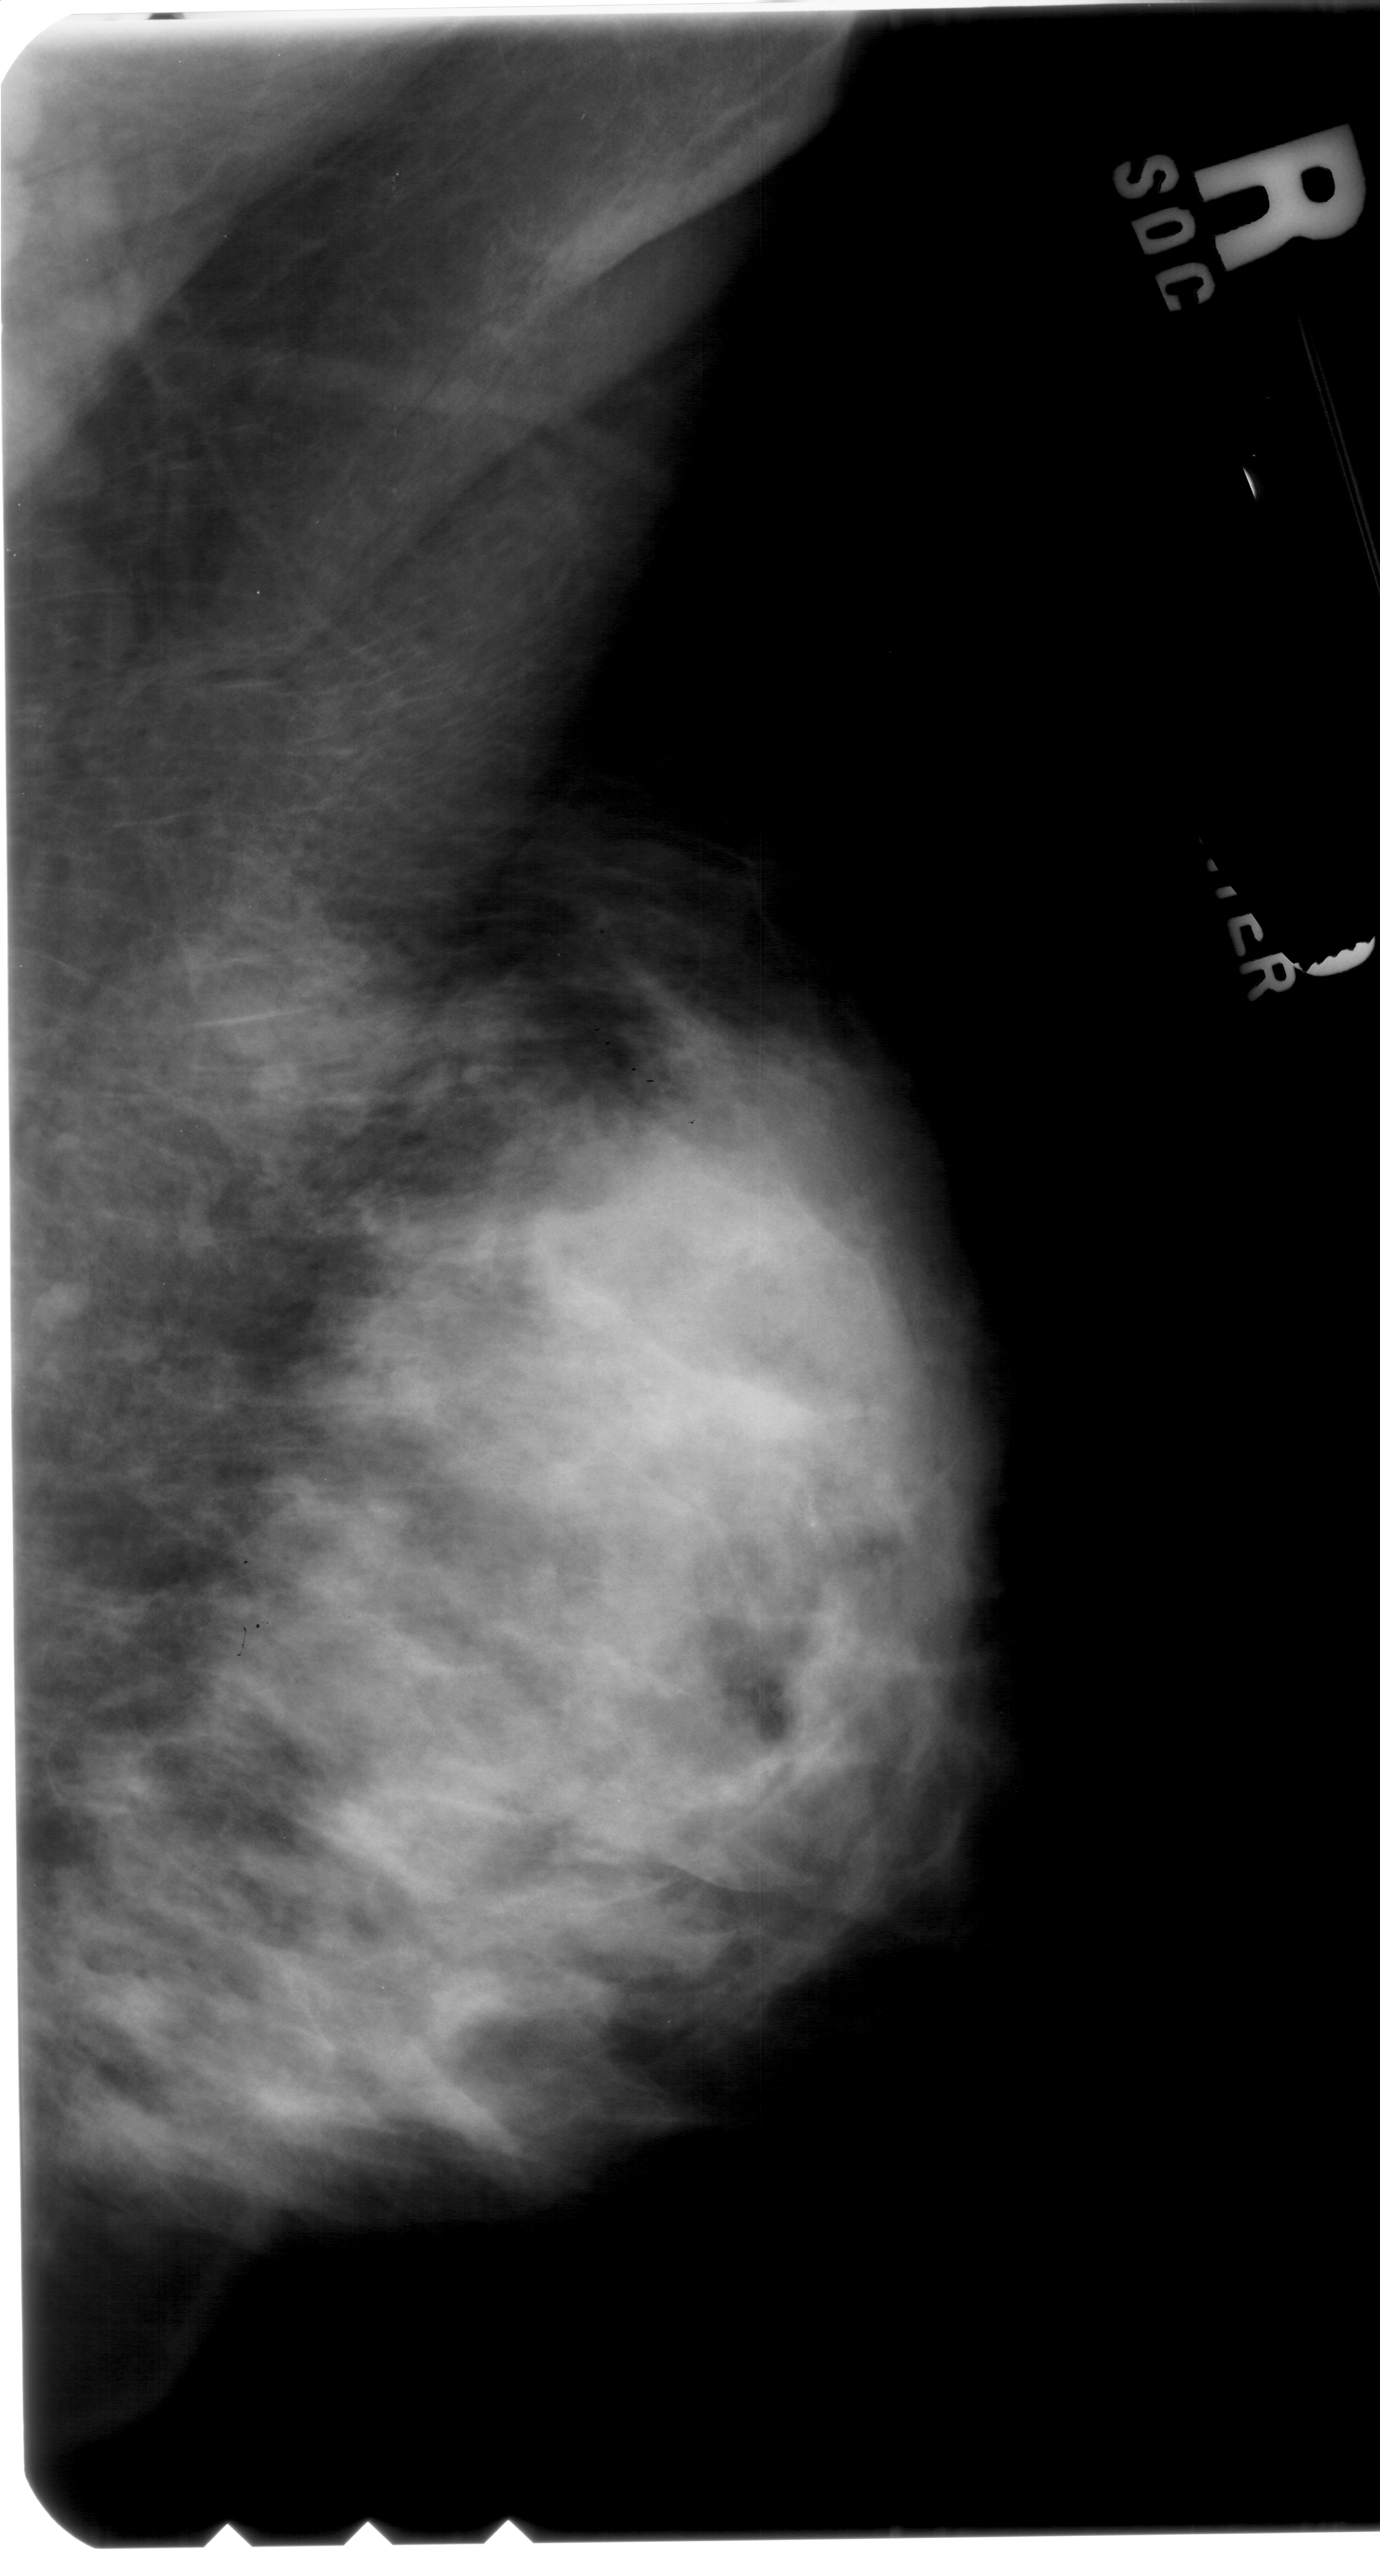
Scanned film-screen mammogram; right breast; mediolateral oblique (MLO) view; BI-RADS breast density category 4 (scale 1–4).
- Calcifications, morphology punctate, distribution clustered; BI-RADS assessment category 4; pathology result (as recorded, not read from the image): benign.